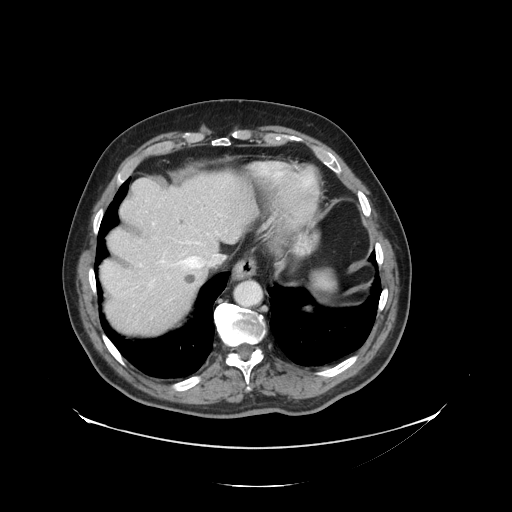
Contrast-enhanced abdominal CT, one axial slice. Position 113 of 138 along the scan axis. Soft-tissue window (W 400 / L 40 HU). 512 × 512 image matrix, field of view 497 × 497 mm. Male patient, age 77 years. From the clinical record (not read from this slice): diagnosis: colorectal cancer liver metastases, imaged before liver resection; multiple liver metastases: no; largest metastasis: 1.5 cm.
Outlined on this slice (expert manual segmentation):
- hepatic veins: box from (x=139, y=211) to (x=222, y=287) px
- liver: (x=102, y=172)–(x=254, y=335)
- planned liver remnant (the part of the liver to remain after resection): (x=102, y=172)–(x=255, y=290)
- liver metastasis: (x=184, y=275)–(x=197, y=285)